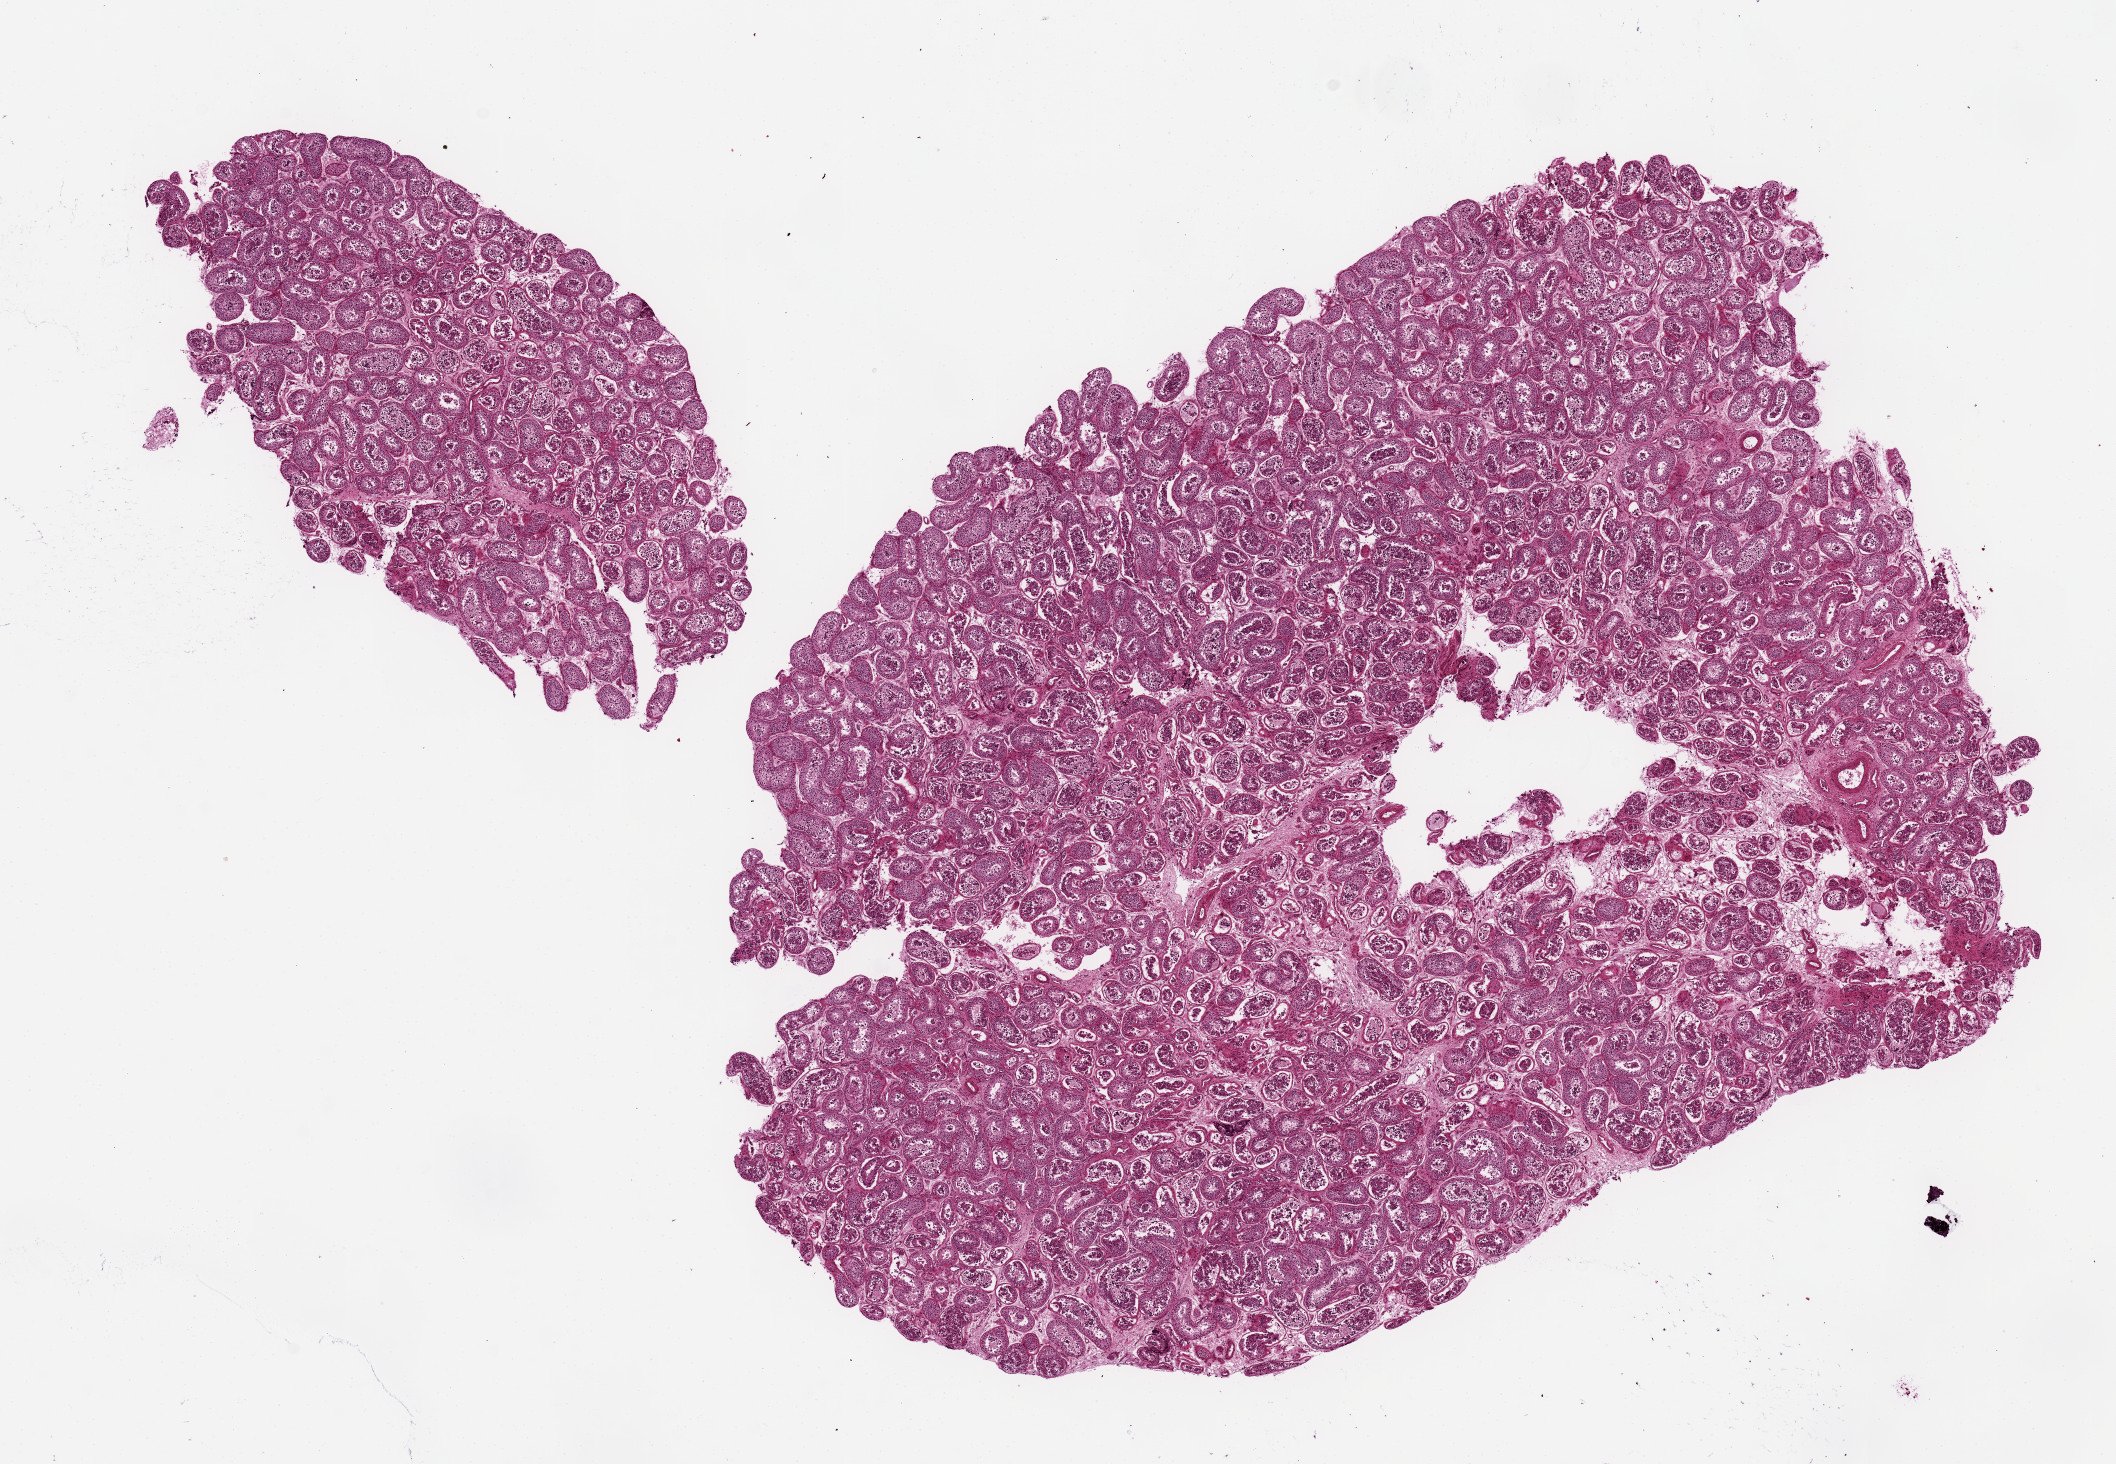
H&E whole-slide image — a low-resolution overview of the entire scanned area, about 16.7 x 11.6 mm; PAXgene-fixed paraffin-embedded (PFPE) section; target tissue: testis; donor tissue sample. Donor sex: male.
Pathologist's review note for this sample: 2 pieces.